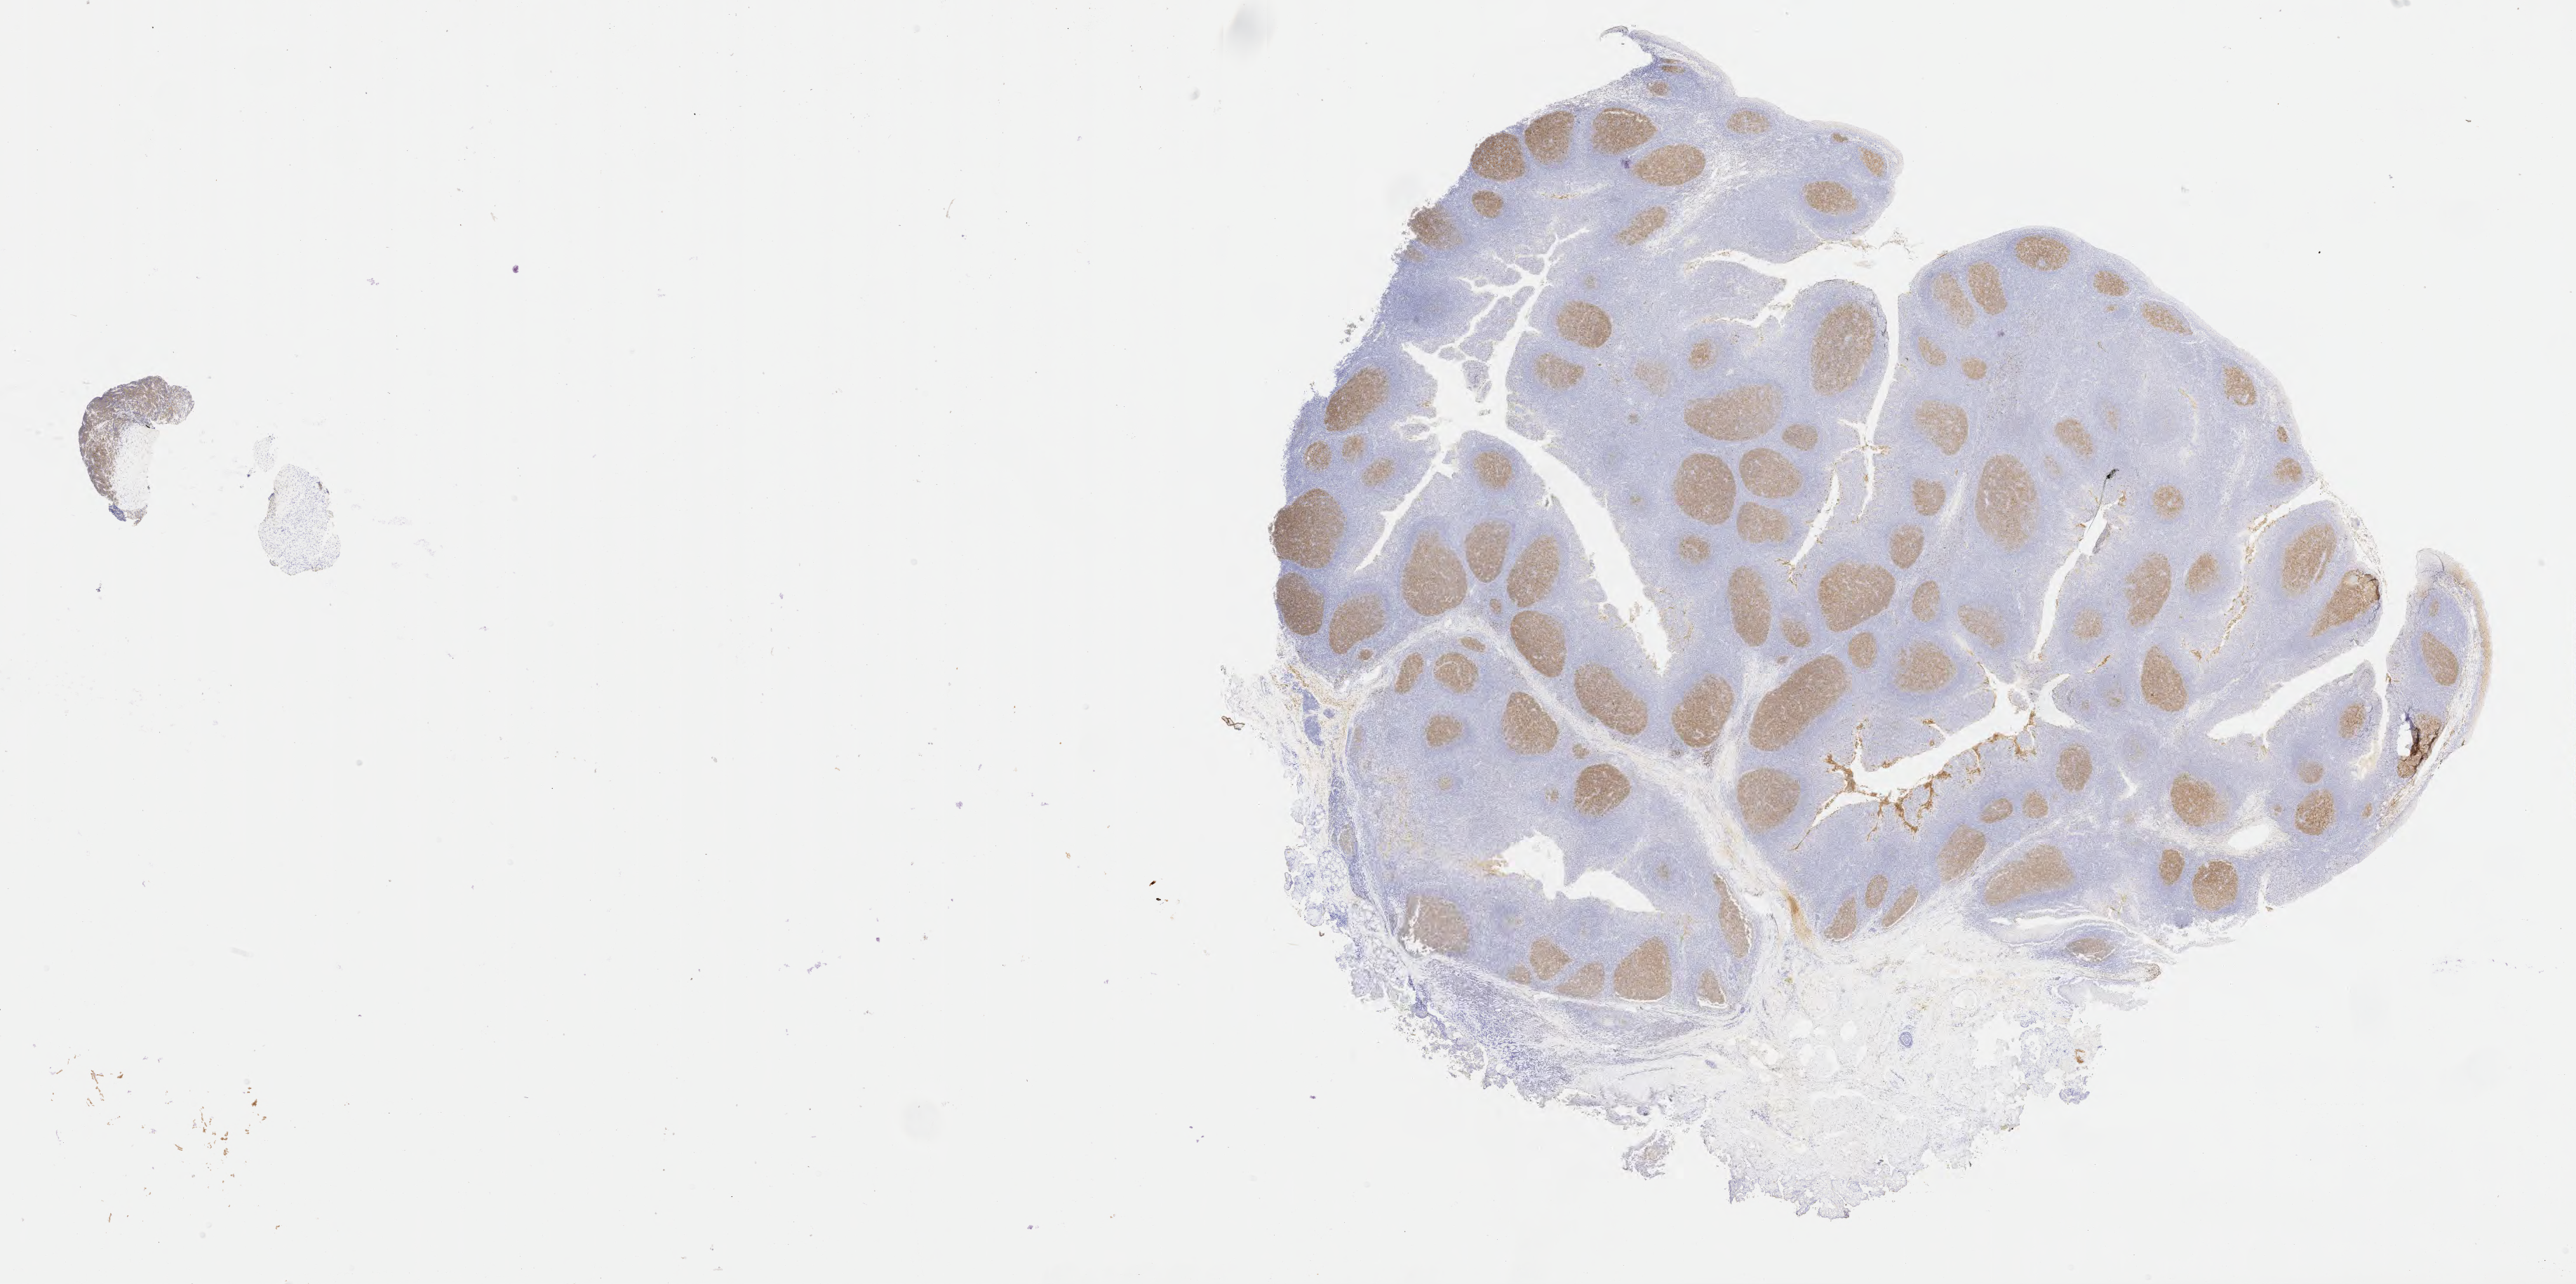
Whole-slide image, immunohistochemical stain for CD10 — low-resolution overview of the scanned area, about 29.7 x 14.8 mm. Tumor tissue. Site: abdomen proper. Female patient; age at initial diagnosis 6 years.
• histologic diagnosis: Diffuse large B-cell lymphoma, NOS